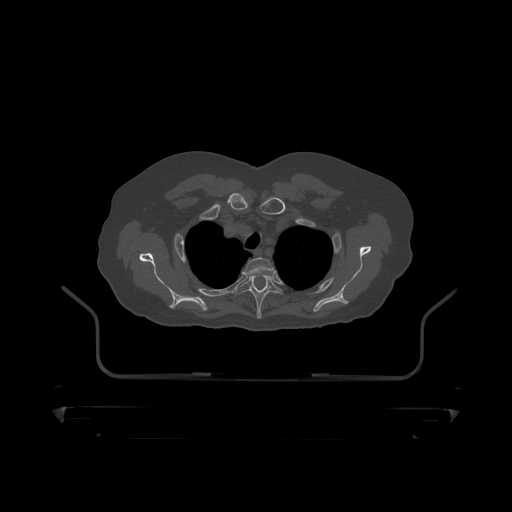
CT including the spine, one axial slice. Slice 362 of 390 in the series (ordered by position). 120 kVp. Bone window (W 1800 / L 400 HU). 1.25 mm slice thickness. 512 × 512 image matrix. Patient: male, 60 years. Case-level facts recorded for this patient, not image findings: primary cancer: prostate.
Structures marked on this image (semi-automatic segmentation, software-assisted and operator-edited):
- T2 vertebra: bounding box (x1, y1, x2, y2) in pixels: (245, 258, 274, 275)
- T3 vertebra: (235, 274, 284, 319)